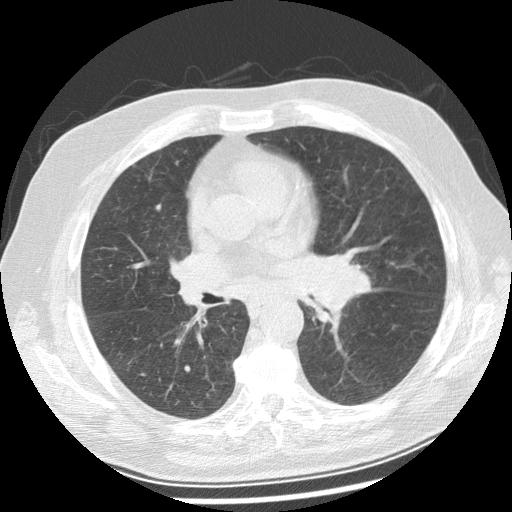
Low-dose screening chest CT, one axial slice; slice 136 of 250 in the series (ordered by position); 120 kVp; lung window (W 1500 / L -600 HU); 512 × 512 image matrix.
Outlined on this slice (outlined manually by an expert reader):
- lesion 1 (tumor, left main bronchus): bounding box [x1, y1, x2, y2] px = [313, 266, 371, 313]